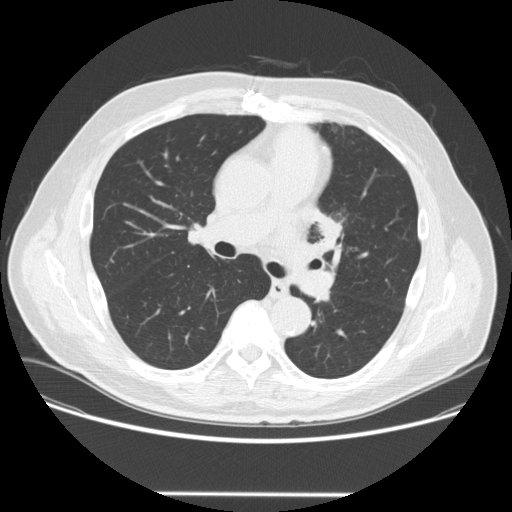
Low-dose screening chest CT, one axial slice; position 156 of 253 along the scan axis; 120 kVp; lung window (W 1500 / L -600 HU); 512 × 512 image matrix.
Structures marked on this image (expert manual segmentation):
- lesion 1 (tumor, upper lobe of left lung): box from (x=320, y=219) to (x=342, y=244) px